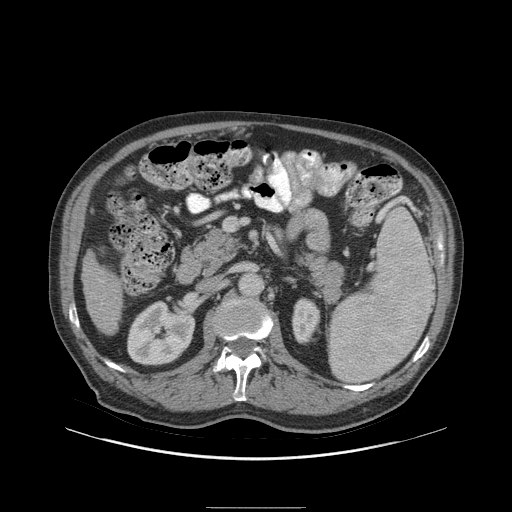
Contrast-enhanced abdominal CT (liver protocol), one axial slice. Position 32 of 105 along the scan axis. Soft-tissue window (W 400 / L 40 HU). 512 × 512 image matrix, field of view 440 × 440 mm. From the clinical record (not read from this slice): diagnosis: hepatocellular carcinoma (patient treated with transarterial chemoembolisation; whether this scan precedes or follows treatment is not stated here); TNM stage (as recorded): Stage-I; Child-Pugh class: A; tumour size: 5.1 cm.
Outlined on this slice (semi-automatically segmented with operator editing):
- liver parenchyma outside the tumour (the mass and vessels are separate outlines, so this box may not span the whole liver): bounding box (x1, y1, x2, y2) in pixels: (80, 250, 122, 334)